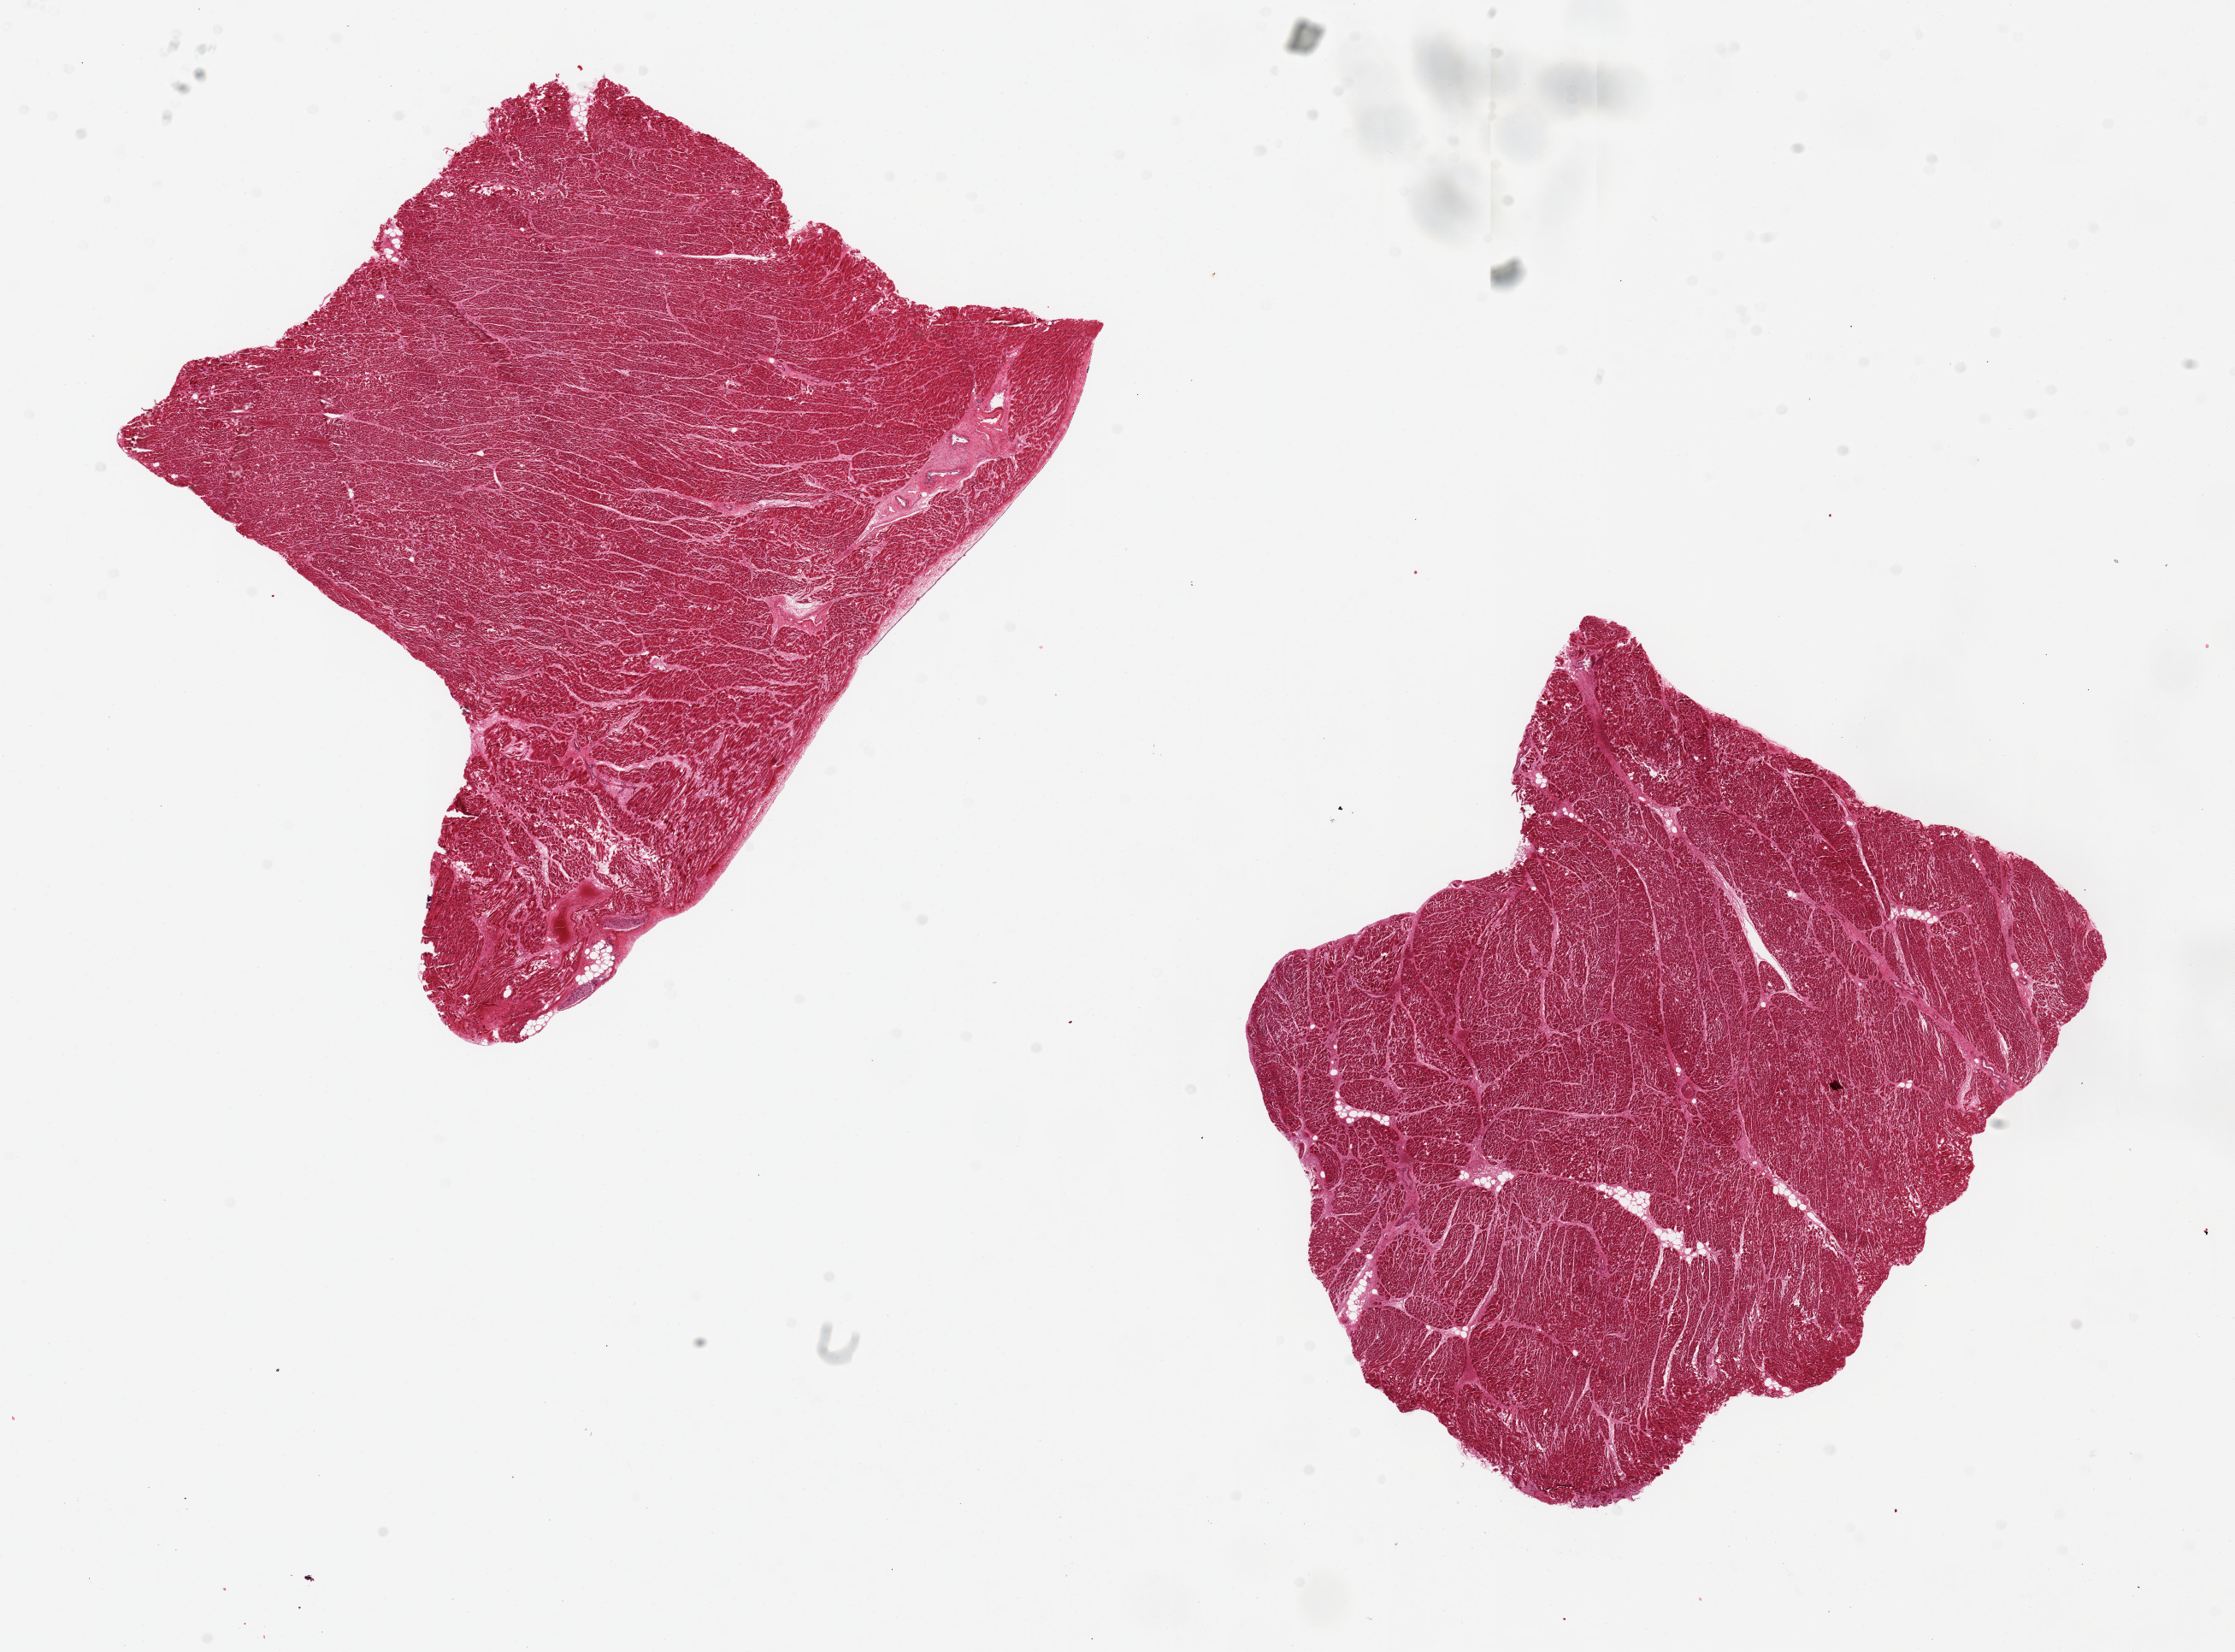
Digitized H&E-stained section — shown as a low-resolution overview of the whole scanned area (about 20.7 x 15.3 mm, slide scanned at 20x). PAXgene-fixed, paraffin-embedded tissue. Target tissue: heart. Tissue donor sample.
- pathologist's review note for this sample: 2 pieces ~7x6mm. Minimal ischemic changes noted